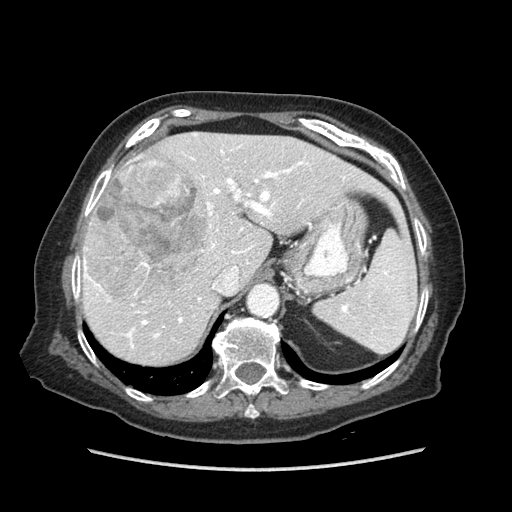
Contrast-enhanced abdominal CT (liver protocol), one axial slice; slice 58 of 89 in the series (ordered by position); reconstruction kernel STANDARD; 140 kVp; soft-tissue window (W 400 / L 40 HU); 512 × 512 image matrix, field of view 360 × 360 mm. From the clinical record (not read from this slice): diagnosis: hepatocellular carcinoma (patient treated with transarterial chemoembolisation; whether this scan precedes or follows treatment is not stated here); TNM stage (as recorded): Stage-IIIA; Child-Pugh class: A; tumour differentiation: well differentiated.
Annotated regions visible in this slice (semi-automatically segmented with operator editing):
- liver parenchyma outside the tumour (the mass and vessels are separate outlines, so this box may not span the whole liver): box from (x=78, y=132) to (x=388, y=364) px
- mass: (x=85, y=158)–(x=206, y=301)
- liver vessels: (x=78, y=133)–(x=345, y=348)